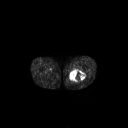
FDG PET of an extremity soft-tissue mass (from a PET/CT study), one axial slice. Slice 251 of 267 in the series (ordered by position). 3.27 mm slice thickness. 128 × 128 image matrix, field of view 700 × 700 mm. Patient: male, 44 years. Case-level facts recorded for this patient, not image findings: histological type: undifferentiated pleomorphic liposarcoma; grade: high; site of the primary tumour: left thigh.
Outlined on this slice (expert contour drawn on MRI and transferred to this co-registered scan by the dataset authors):
- gross tumour volume including surrounding oedema: box from (x=68, y=69) to (x=86, y=83) px
- gross tumour volume (mass): (x=70, y=70)–(x=85, y=81)